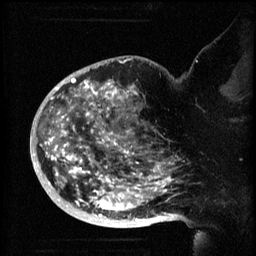
Breast MRI (dynamic contrast-enhanced), one sagittal slice; slice 42 of 60 in the series (ordered by position); 3 images stored at this slice position (order not interpretable as contrast timing); 1.5 T; TE 4.2 ms, TR 8.2 ms; 256 × 256 image matrix, field of view 200 × 200 mm. Patient: female, 50 years.
Structures marked on this image (semi-automatically segmented with operator editing):
- analysis volume of interest (the breast-tissue region the enhancement analysis was run in; not a lesion): bounding box (x1, y1, x2, y2) in pixels: (44, 72, 173, 219)
- tumour enhancement mask (voxels above the 70 % enhancement threshold inside the analysis volume of interest): (45, 78, 173, 219)